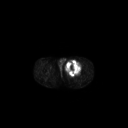
FDG PET of an extremity soft-tissue mass (from a PET/CT study), one axial slice. Position 250 of 267 along the scan axis. 128 × 128 image matrix, field of view 700 × 700 mm. Male patient, age 63 years. From the clinical record (not read from this slice): histological type: pleiomorphic liposarcoma; grade: high; site of the primary tumour: left thigh.
Annotated regions visible in this slice (expert contour drawn on MRI and transferred to this co-registered scan by the dataset authors):
- gross tumour volume including surrounding oedema: bounding box <65,60,82,75> (left, top, right, bottom; pixels)
- gross tumour volume (mass): <65,60,81,75>